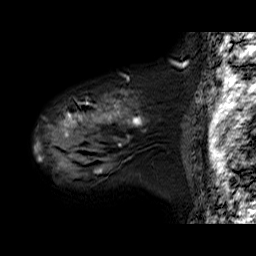
Breast MRI (dynamic contrast-enhanced), one sagittal slice; position 52 of 60 along the scan axis; dynamic contrast-enhanced series, time point 2 of 6 at this slice position (early post-contrast); 1.5 T; TE 6.3 ms, TR 32.9 ms; 256 × 256 image matrix, field of view 200 × 200 mm. Female patient. From the clinical record (not read from this slice): setting: breast cancer imaged before/during neoadjuvant chemotherapy; receptor status: HER2-positive.
Outlined on this slice (semi-automatic segmentation, software-assisted and operator-edited):
- analysis volume of interest (the breast-tissue region the enhancement analysis was run in; not a lesion): bounding box <36,90,149,180> (left, top, right, bottom; pixels)
- tumour enhancement mask (voxels above the 100 % enhancement threshold inside the analysis volume of interest): <36,102,143,173>